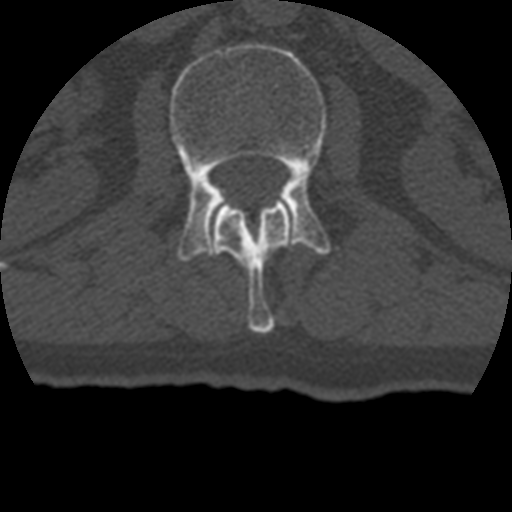
CT including the spine, one axial slice. Reconstruction kernel STANDARD. 120 kVp. Bone window (W 1800 / L 400 HU). 1.25 mm slice thickness. 512 × 512 image matrix, field of view 160 × 160 mm. Patient age 69 years. From the clinical record (not read from this slice): primary cancer: prostate.
Outlined on this slice (semi-automatic segmentation, software-assisted and operator-edited):
- L1 vertebra: bounding box (x1, y1, x2, y2) in pixels: (211, 200, 293, 334)
- L2 vertebra: (170, 43, 331, 261)